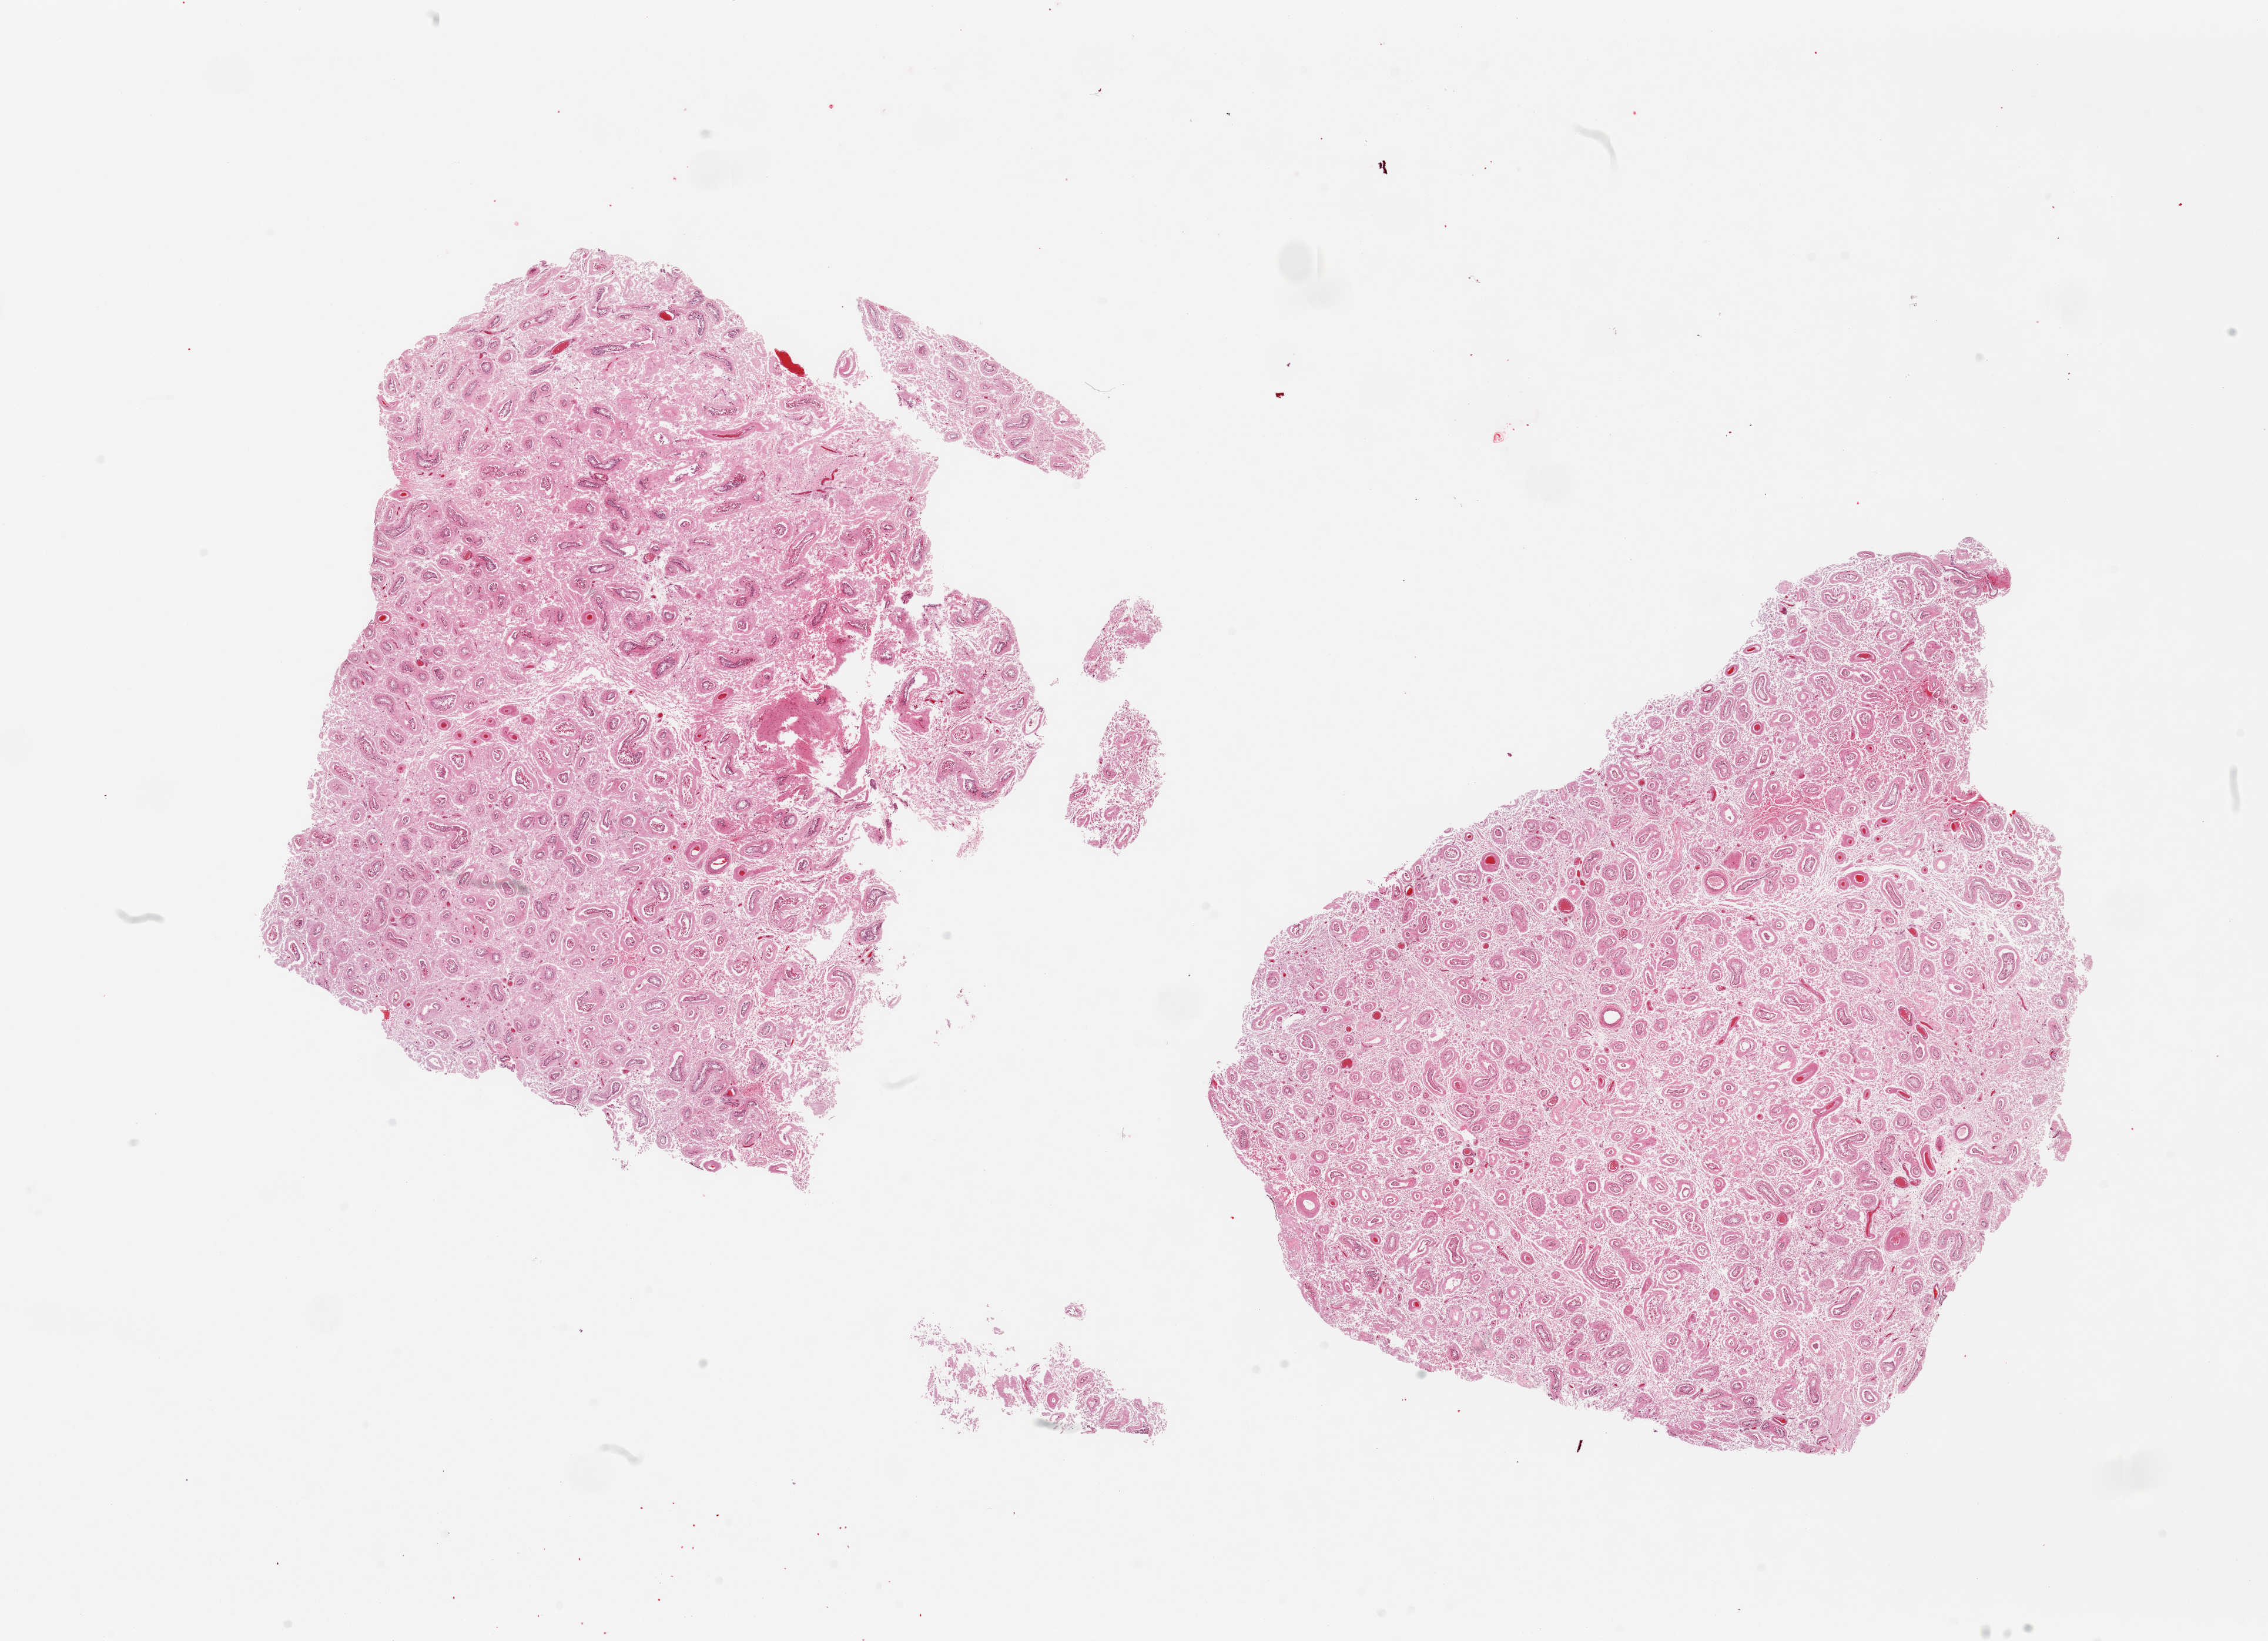
Haematoxylin and eosin whole-slide image — low-resolution overview of the scanned area, about 30.5 x 22.1 mm (from a 20x scan), PAXgene-fixed, paraffin-embedded tissue, section of testis (target tissue), tissue donor sample. Donor sex: male.
Reviewer comment on this tissue sample: 2 pieces, atrophy, moderate-marked tubular autolysis.